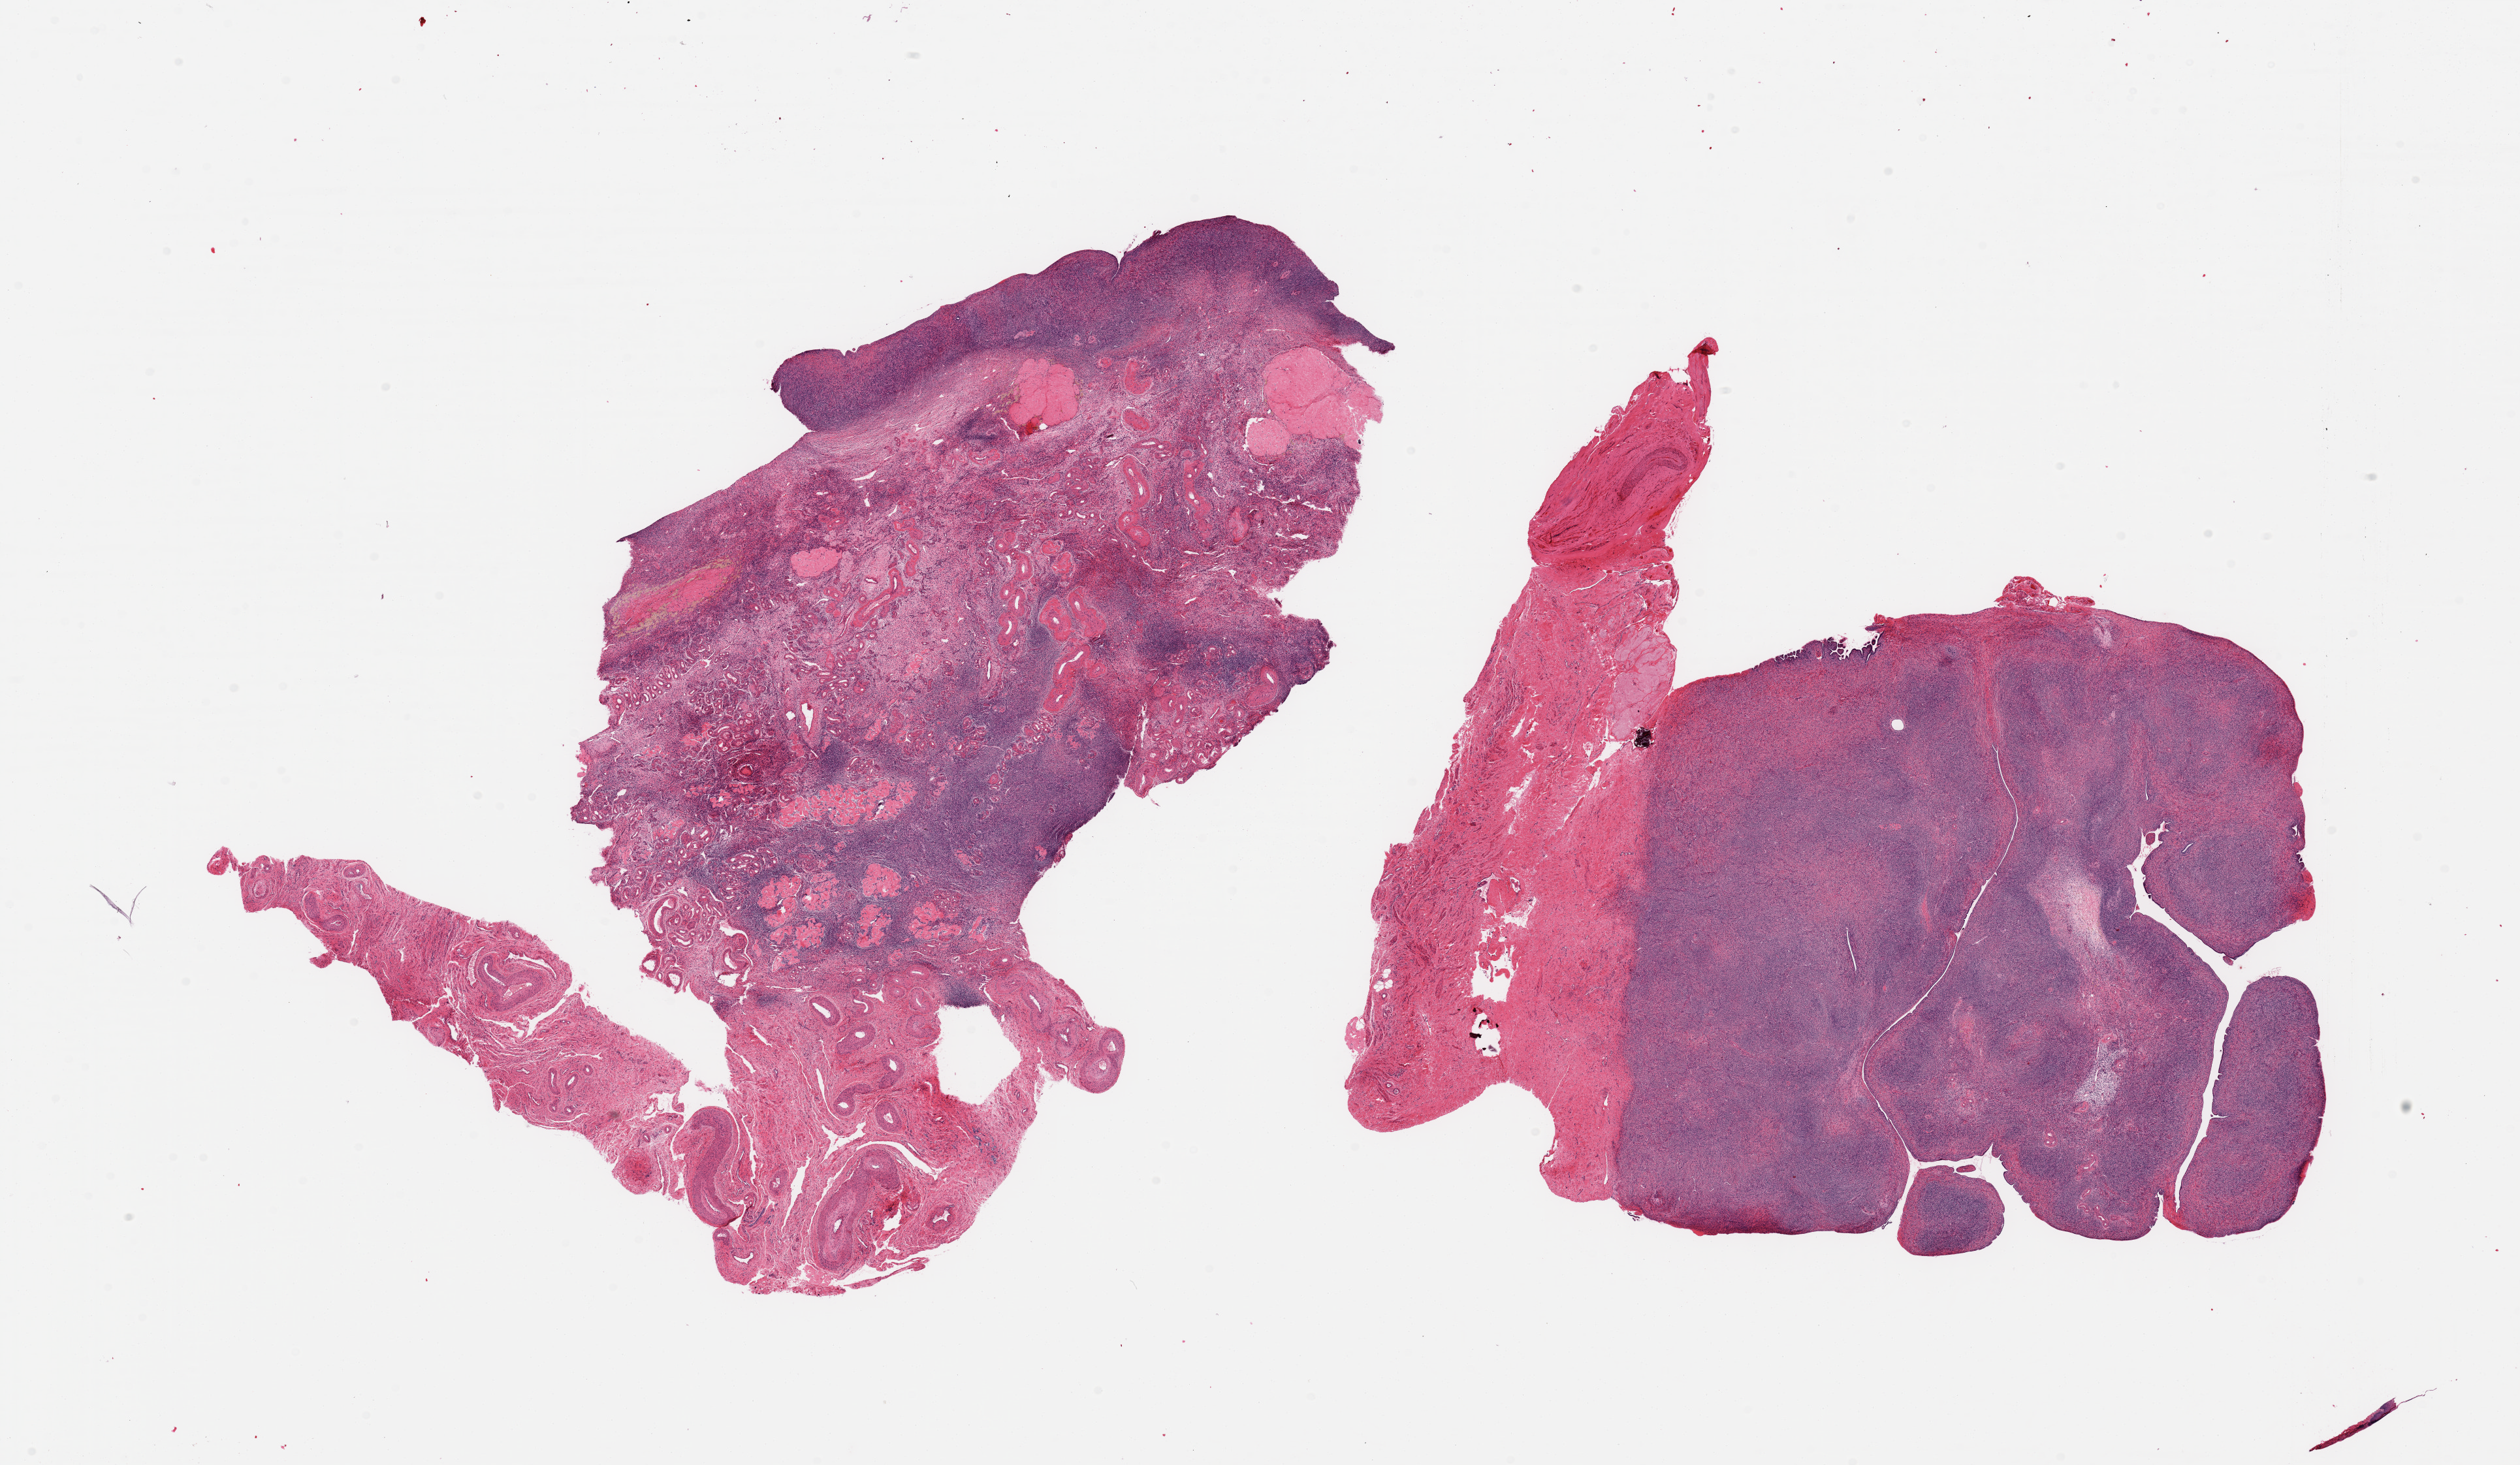
Digitized hematoxylin and eosin (H&E)-stained section, brightfield, a low-resolution overview of the entire scanned area, about 30.5 x 17.7 mm (acquisition: 20x scan); PAXgene-fixed paraffin-embedded (PFPE) section; sampled site (target tissue): ovary; donor tissue sample. Donor: female.
* reviewer comment on this tissue sample: 2 pieces; 1 with numerous corpora albicantia